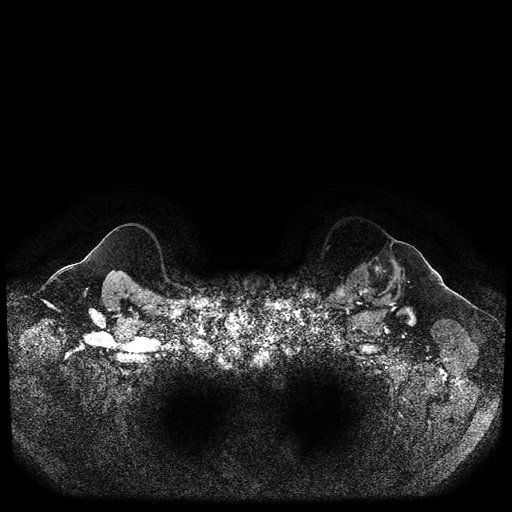
Breast MRI (dynamic contrast-enhanced, multi-phase), one axial slice; dynamic contrast-enhanced series, time point 2 of 5 at this slice position (early post-contrast); 1.5 T; TE 2.6 ms, TR 5.3 ms; 2 mm slice thickness; 512 × 512 image matrix, field of view 350 × 350 mm. Patient: female, 64 years.
Structures marked on this image (semi-automatically segmented with operator editing):
- breast lesion (labelled 'tumour' in the annotation; benign lesions carry a separate 'benign' label): bounding box (x1, y1, x2, y2) in pixels: (359, 249, 410, 307)